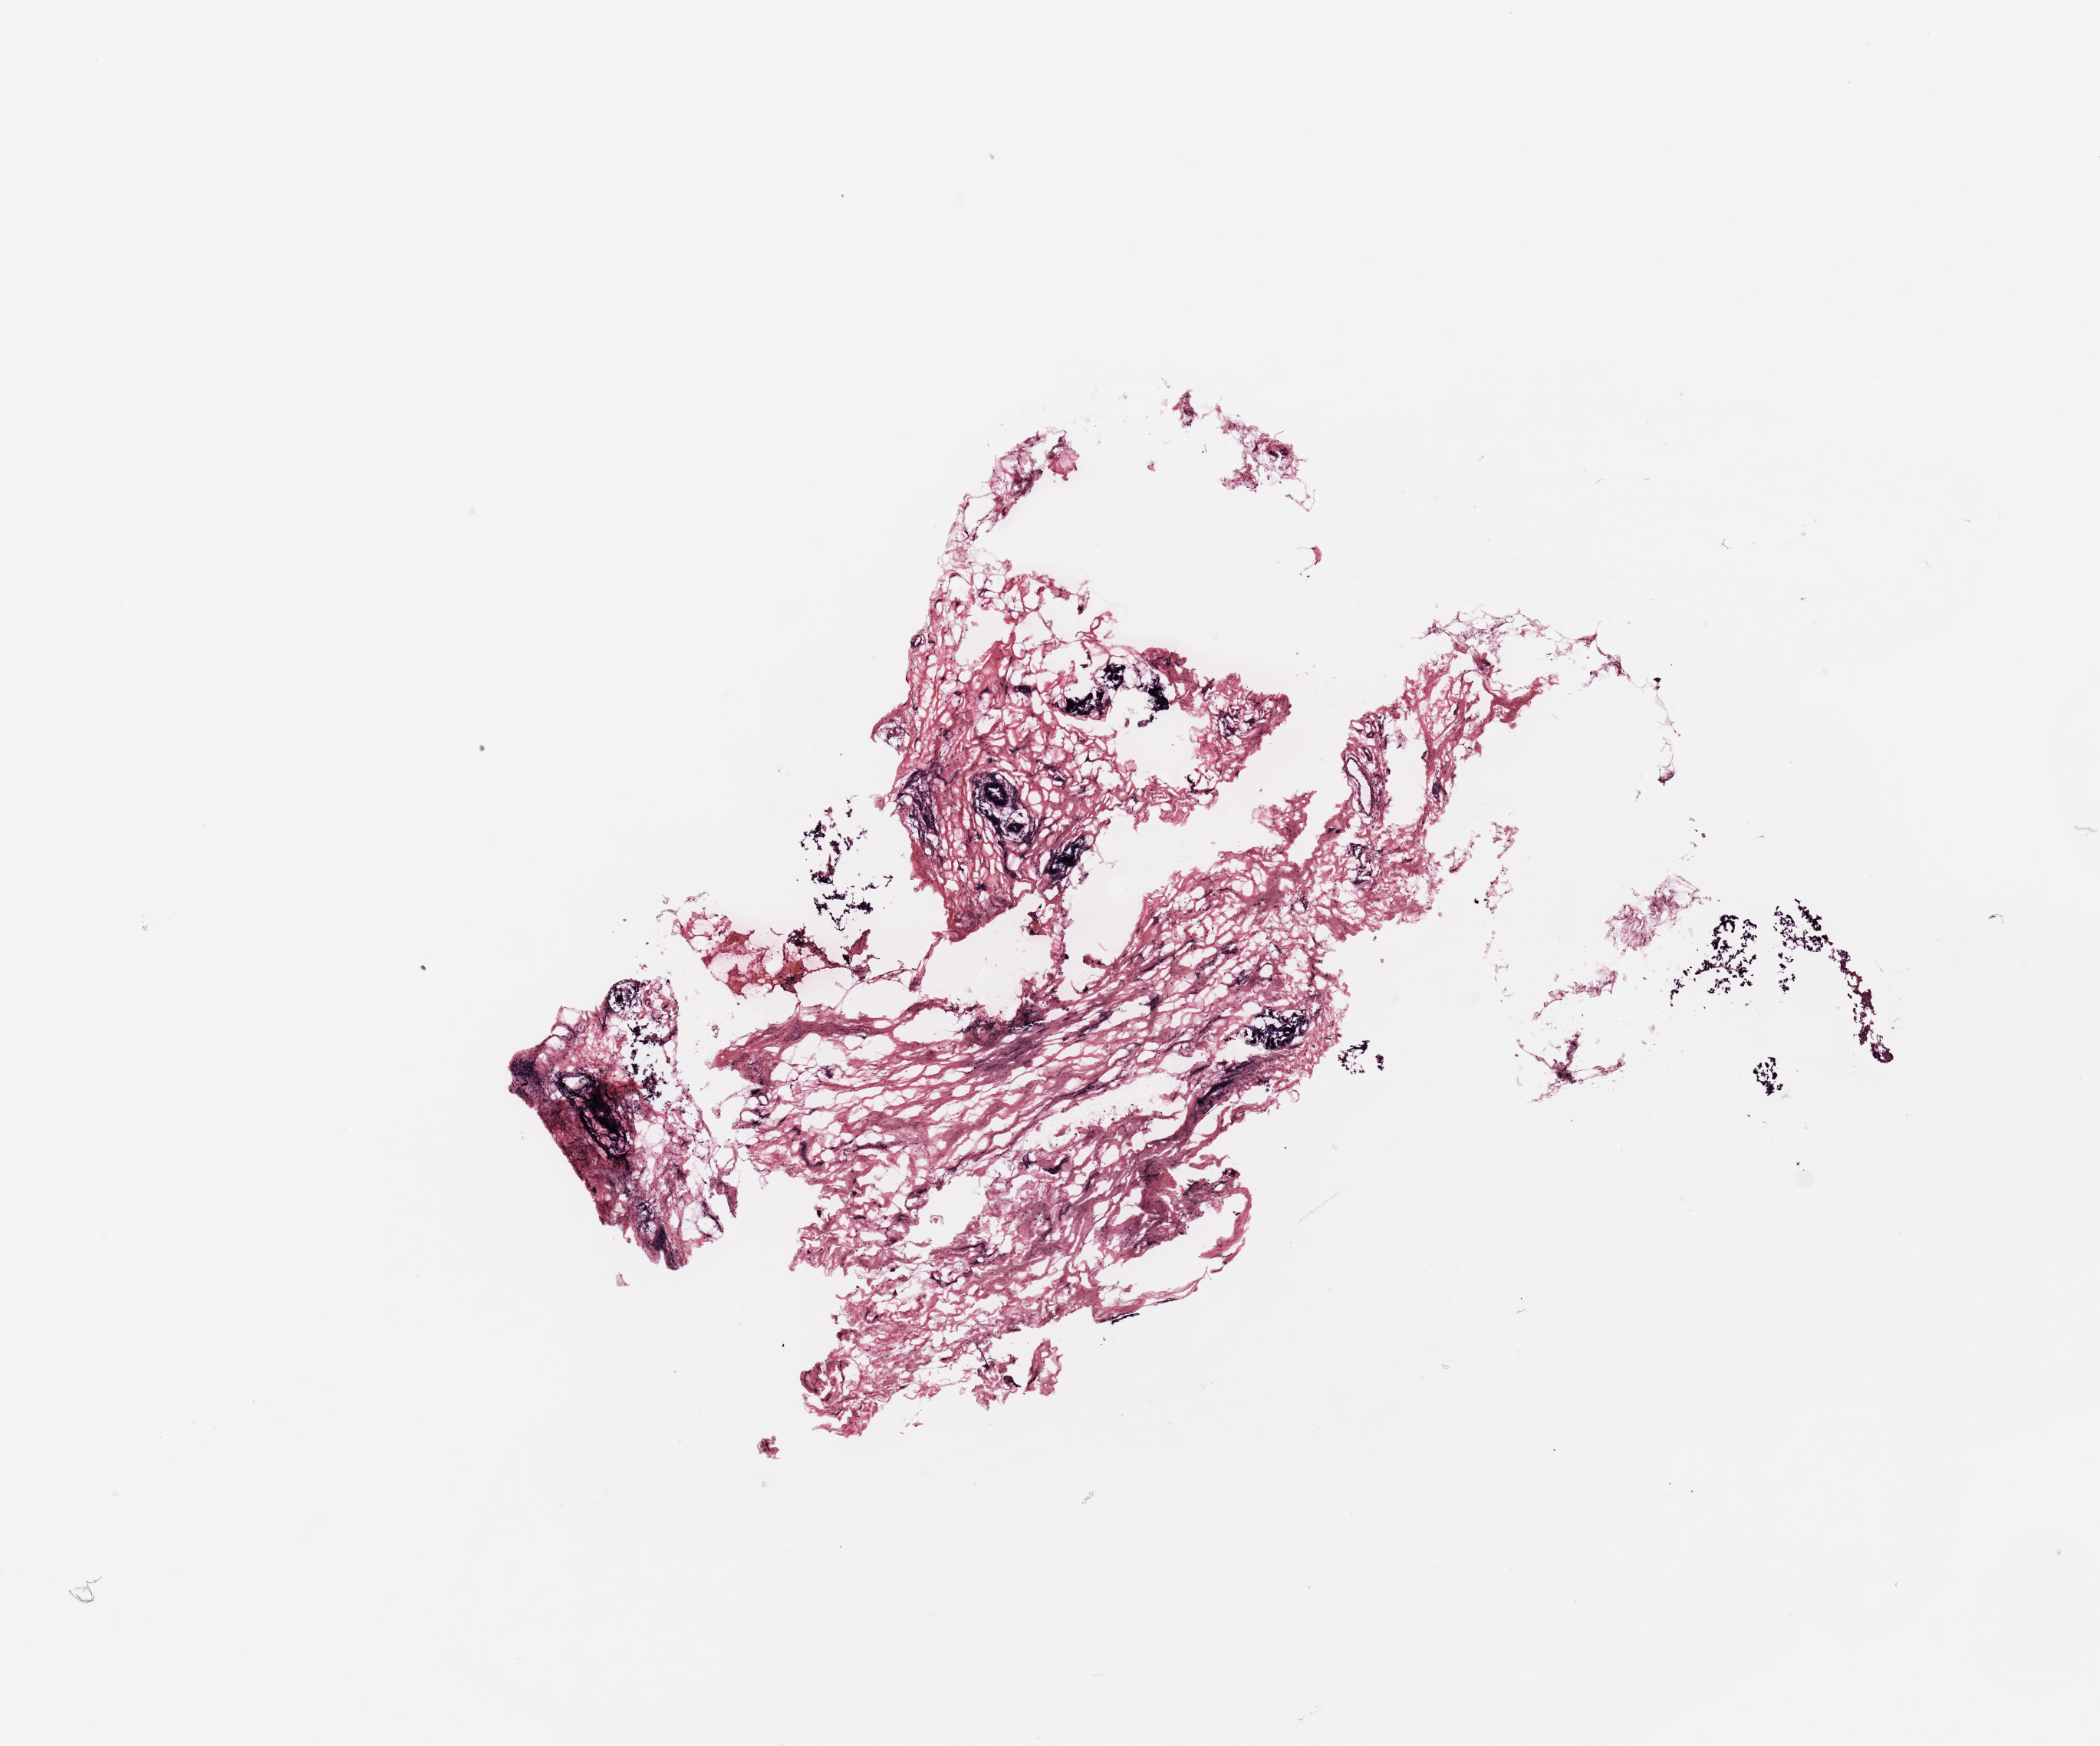
H&E-stained whole-slide image — low-resolution overview of the scanned area, about 10.8 x 9.0 mm (acquisition: 20x scan). Tumour tissue sample, breast. 58-year-old female patient.
Histologic diagnosis: Infiltrating duct carcinoma, NOS. AJCC pathologic stage: II.